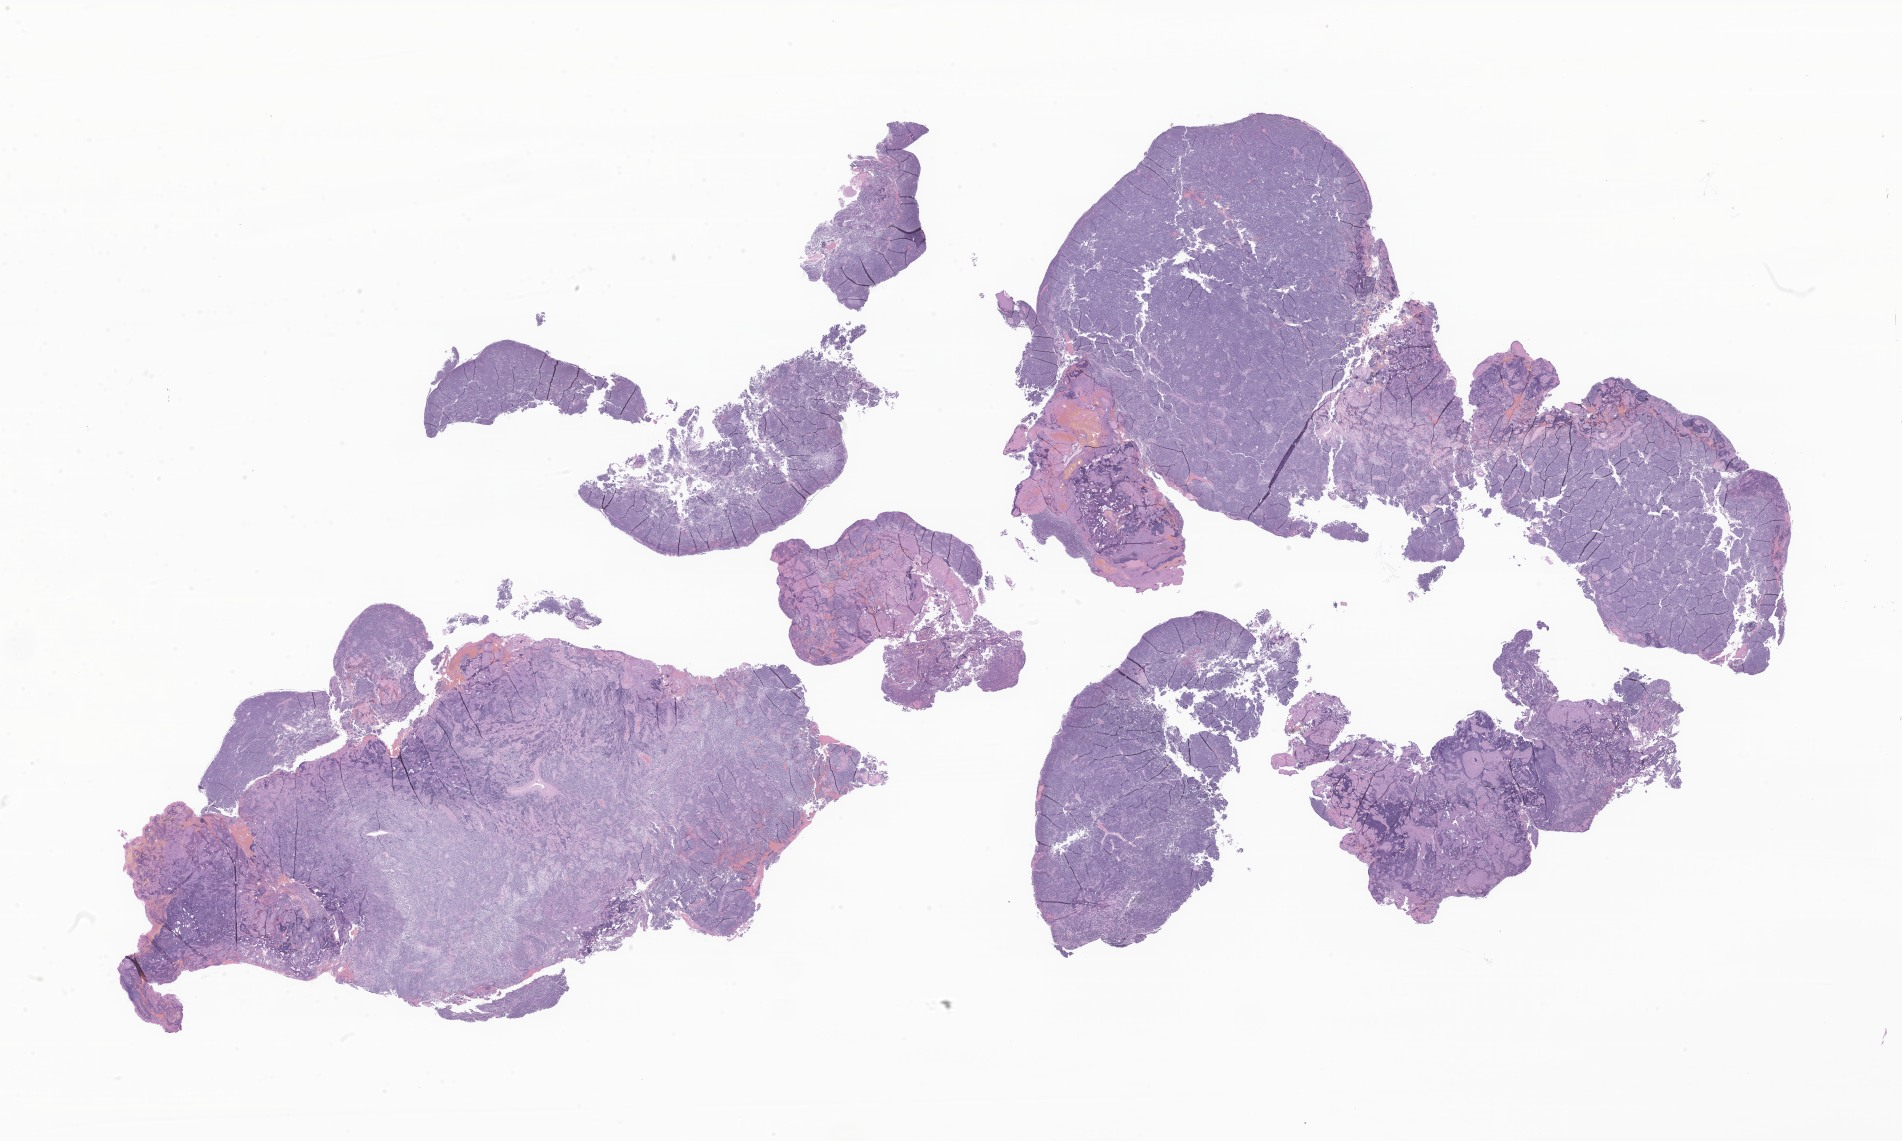
Haematoxylin and eosin whole-slide image of tumor tissue from the brain — a low-resolution overview of the entire scanned area, about 32.1 x 19.2 mm; formalin-fixed, paraffin-embedded (FFPE) tissue. Female patient, age 64 months (5 years 4 months).
* recorded diagnosis: Neoplasm, uncertain whether benign or malignant